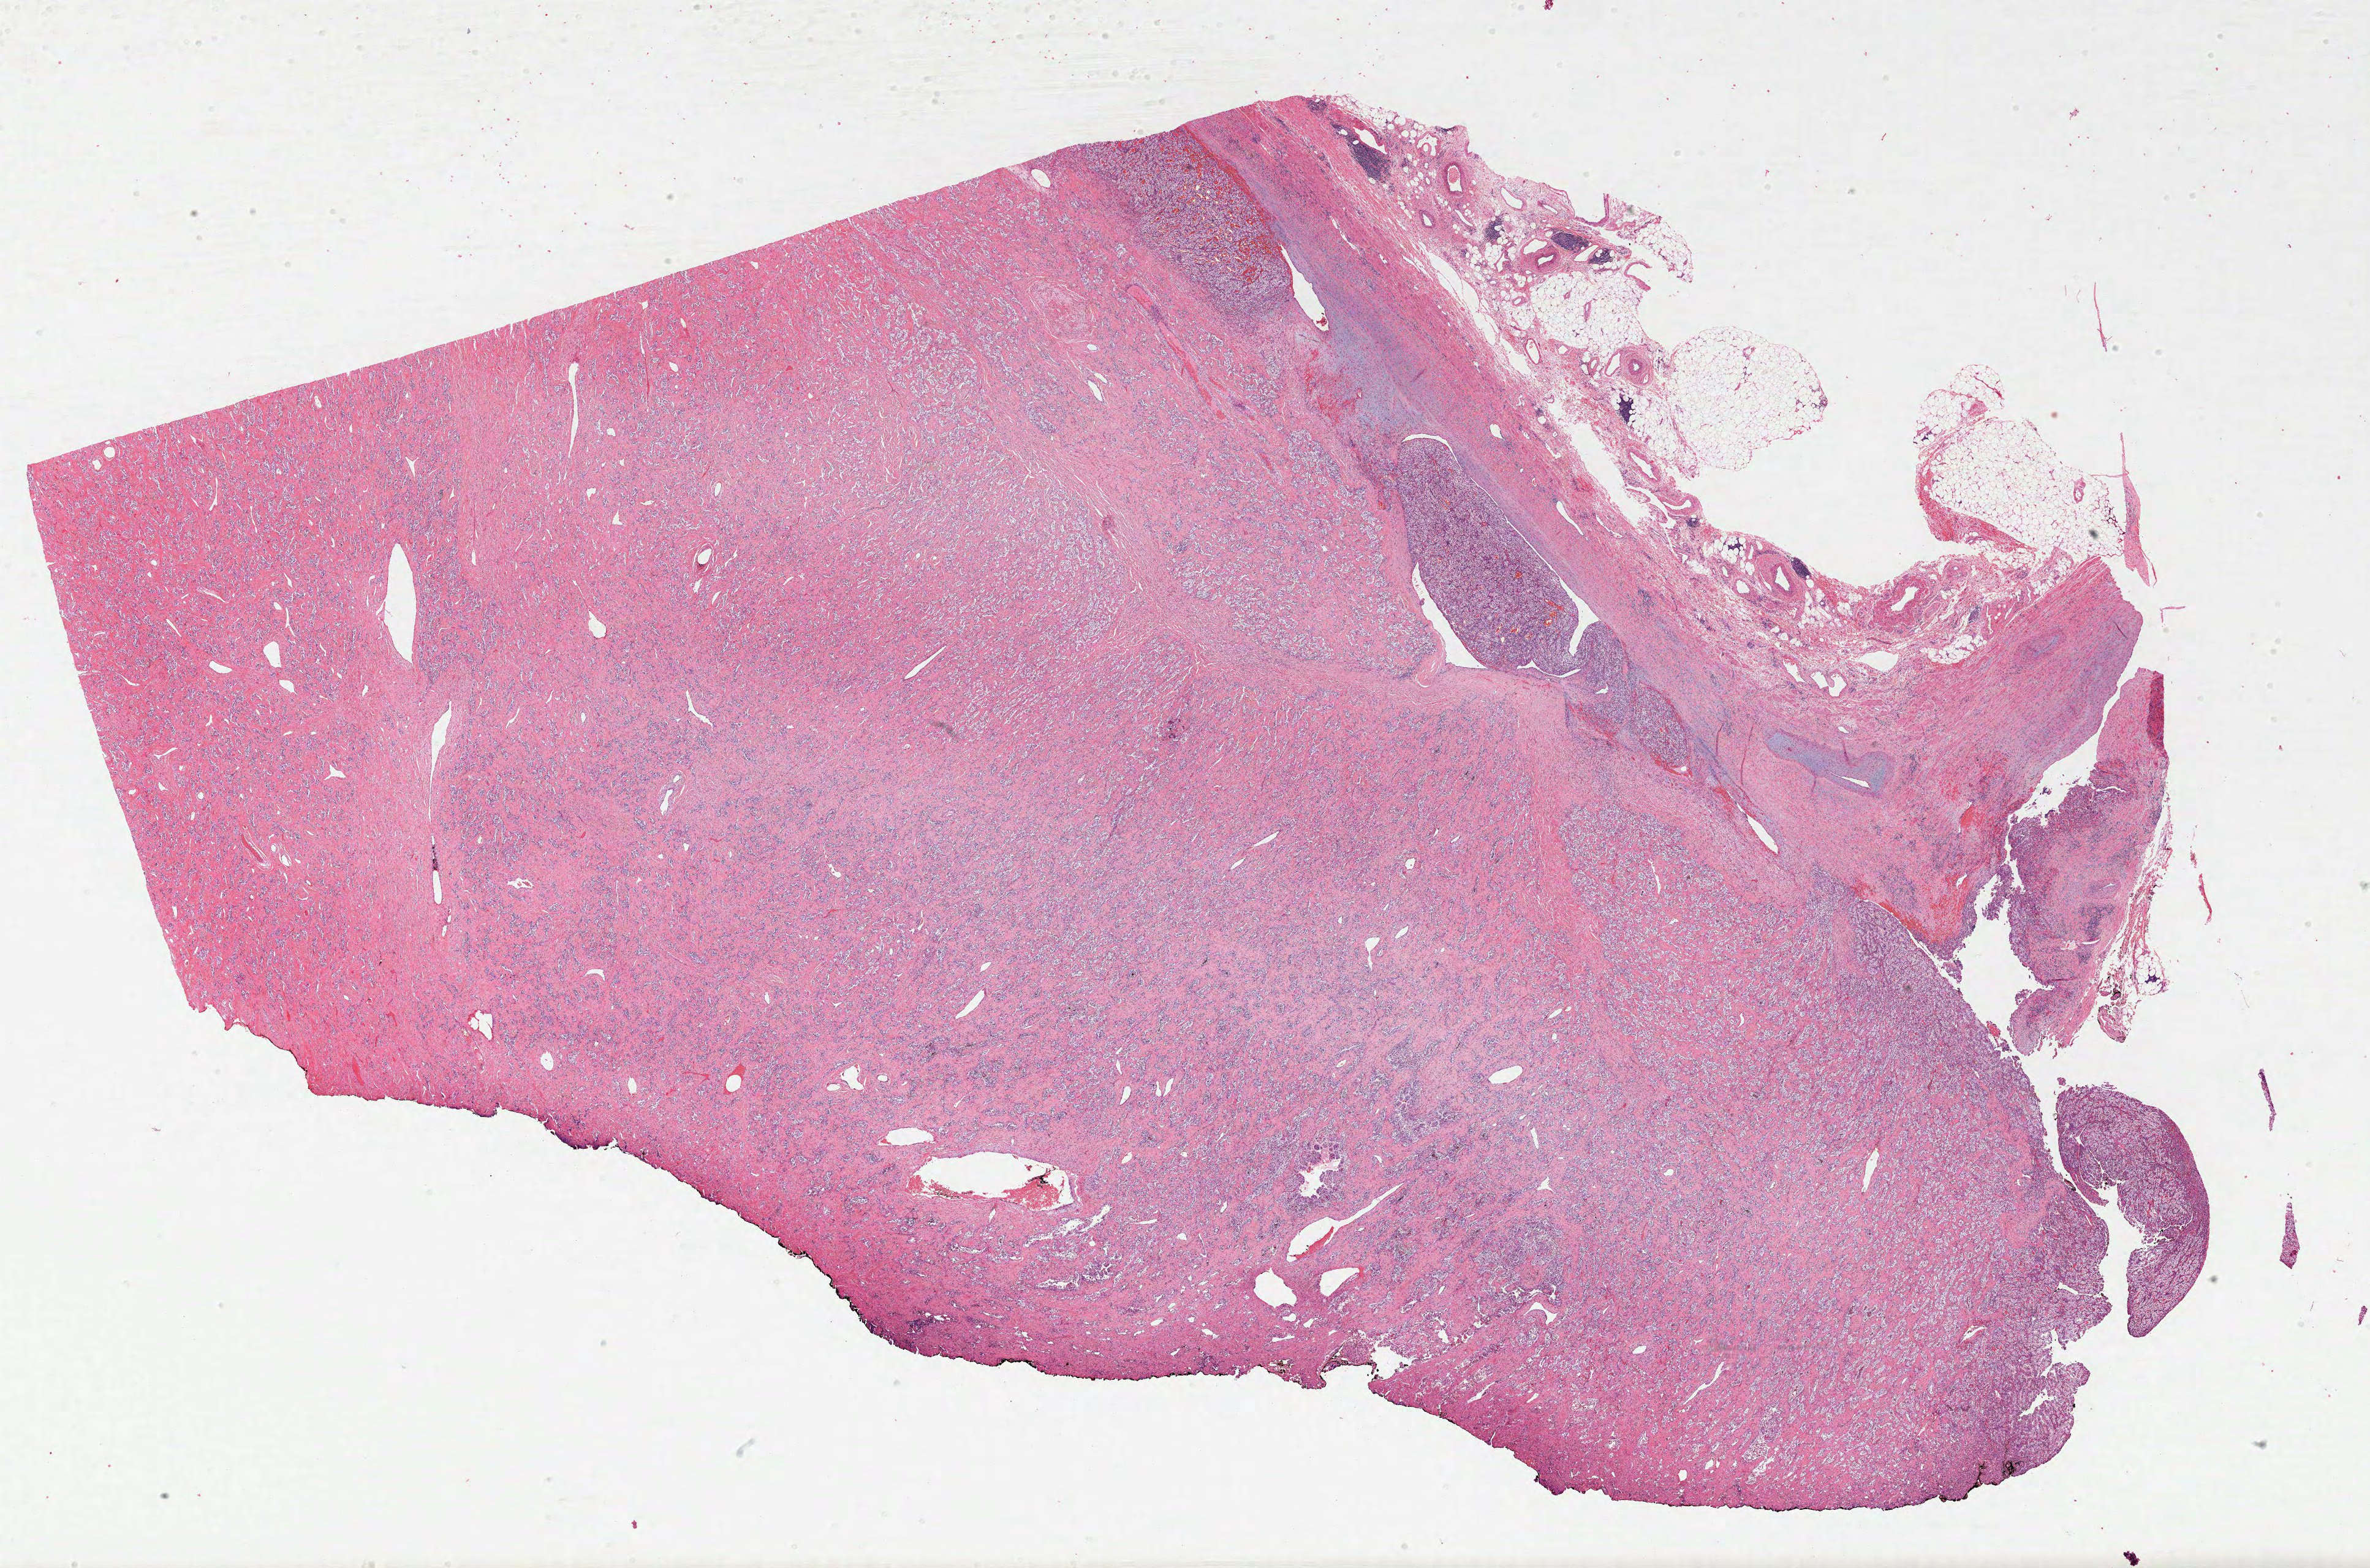
Whole-slide histology image, H&E-stained — a low-resolution overview of the entire scanned area, about 31.2 x 20.6 mm (from a 40x scan); formalin-fixed paraffin-embedded (FFPE) diagnostic section; sample: primary tumour, kidney. Patient: male, age at initial diagnosis 69 years.
Diagnosis: Clear cell adenocarcinoma, NOS.